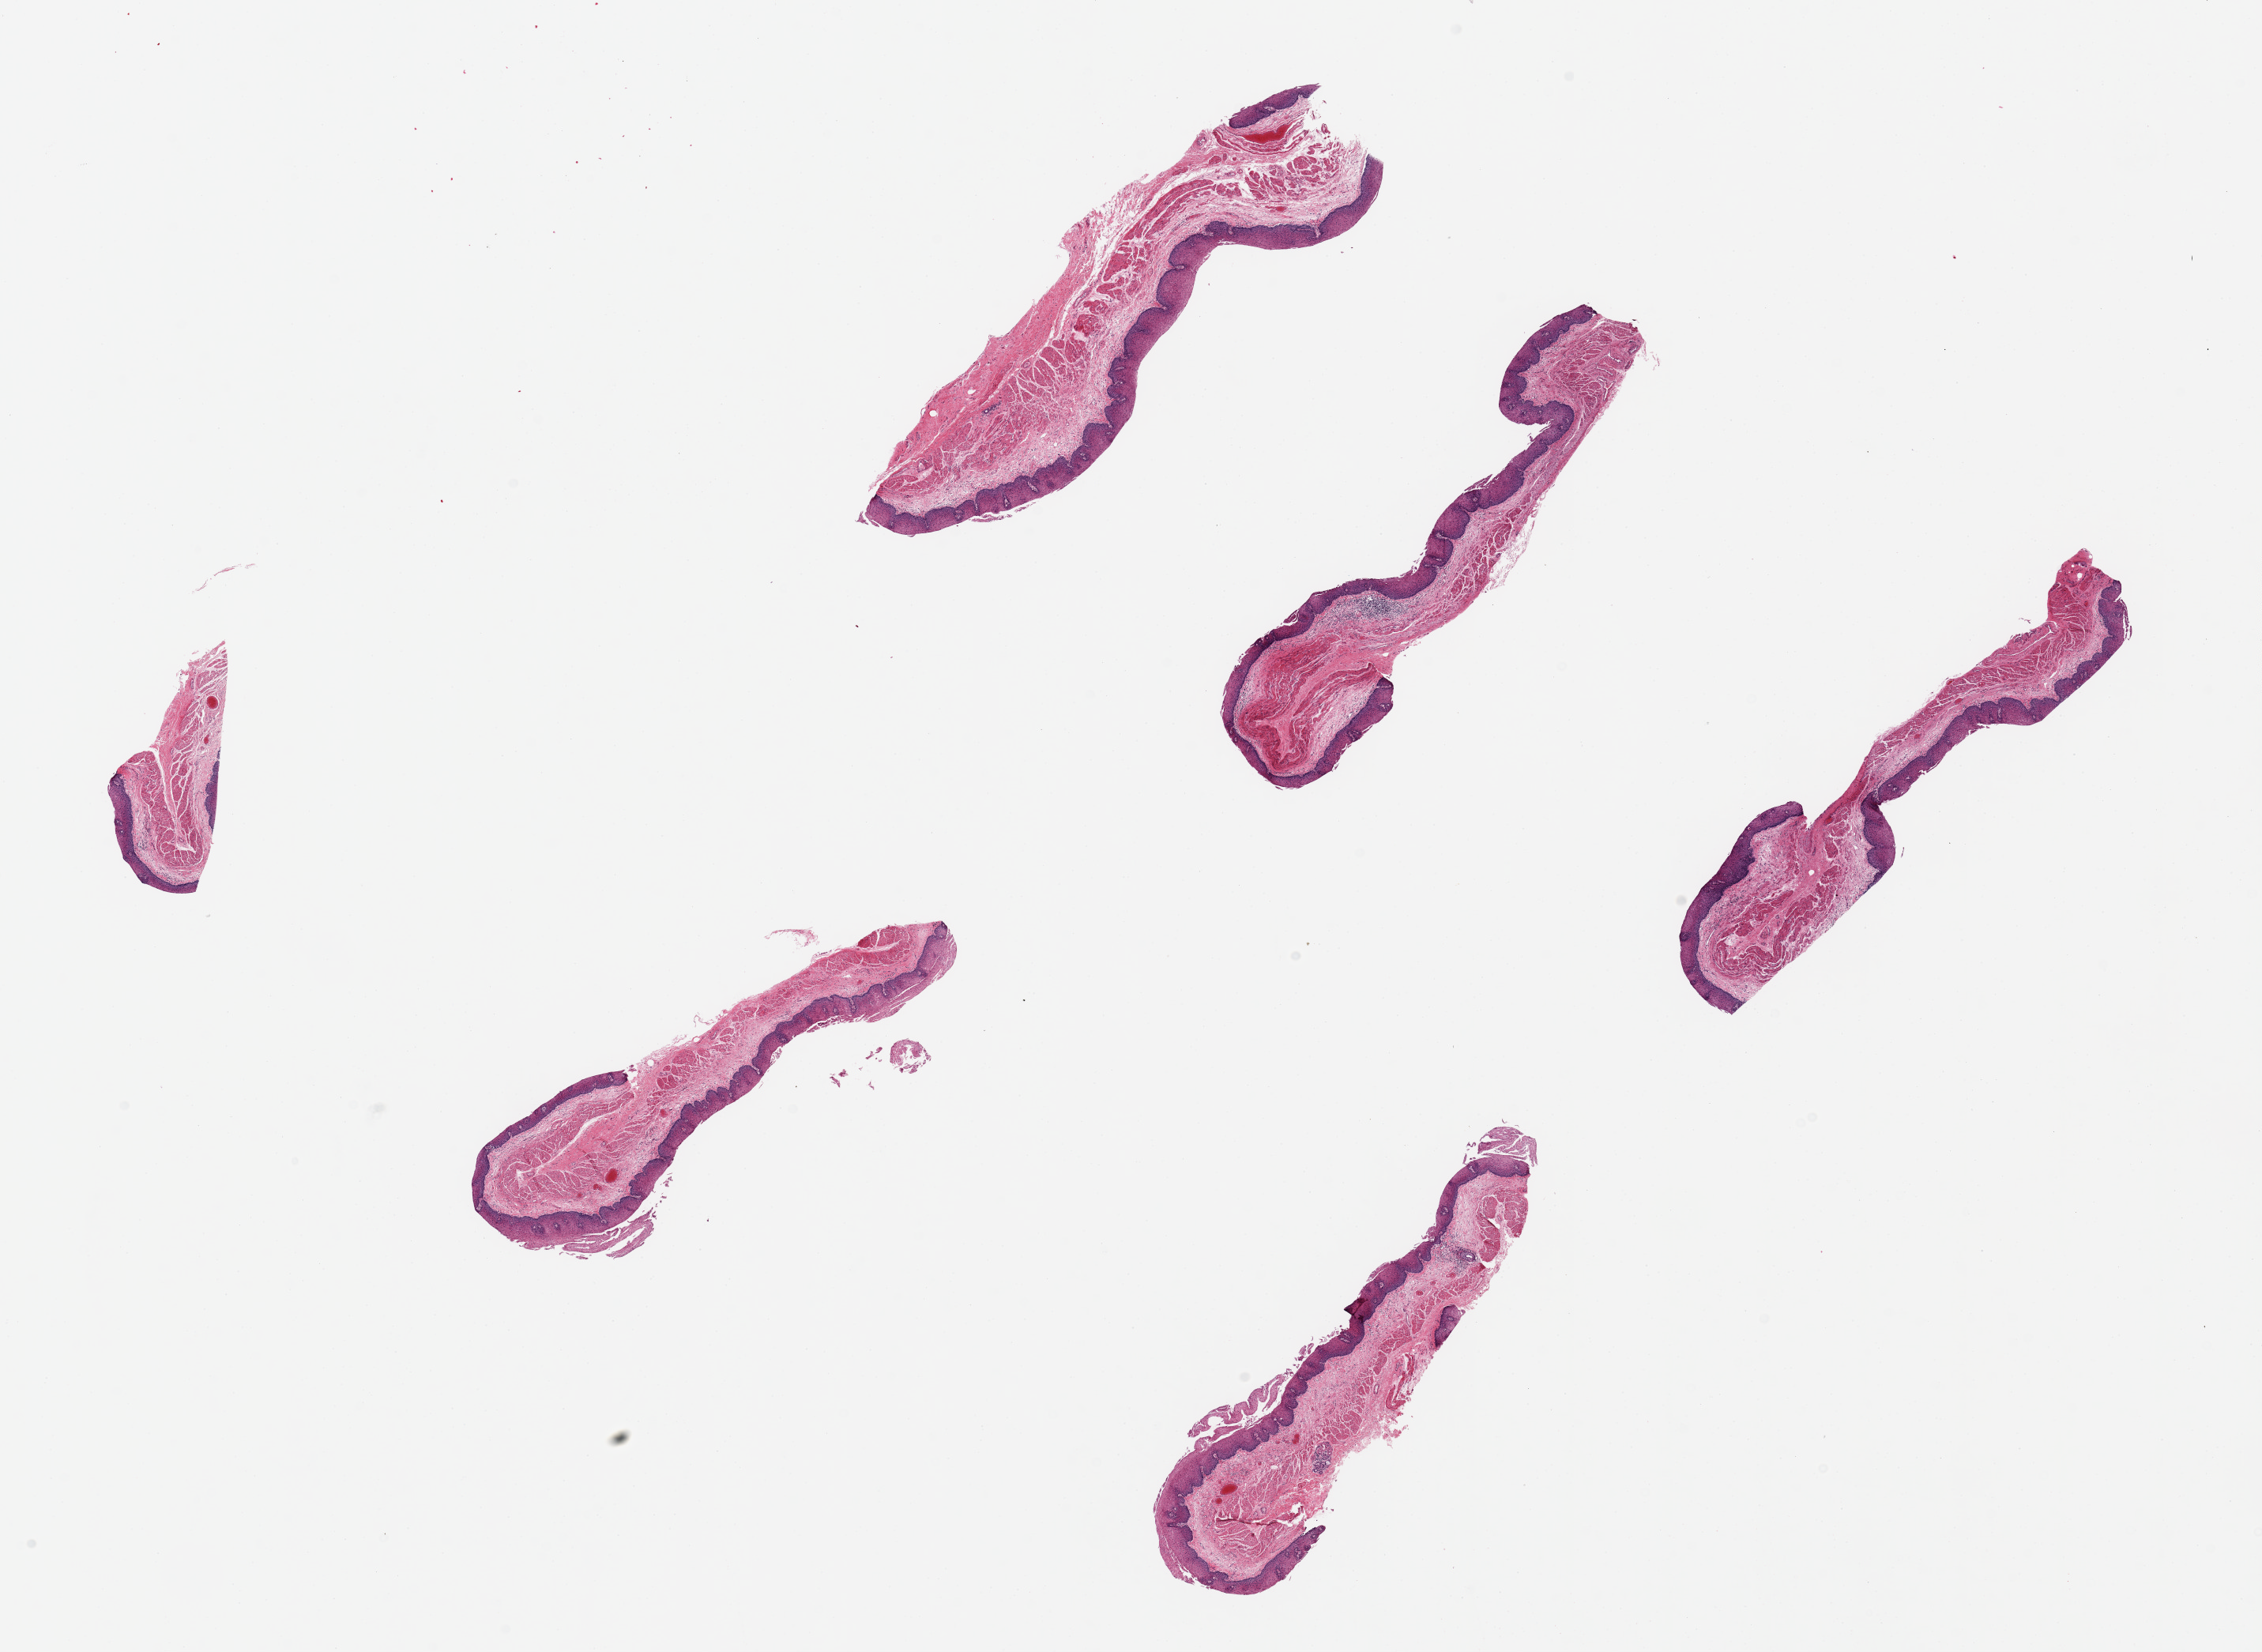
Digitized haematoxylin and eosin-stained section, shown as a low-resolution overview of the whole scanned area (about 22.6 x 16.5 mm); PAXgene-fixed paraffin-embedded (PFPE) section; section of esophageal mucous membrane (target tissue); tissue donor sample.
Reviewer comment on this tissue sample: 6 pieces, up to 6x2mm; good squamous epithelium.